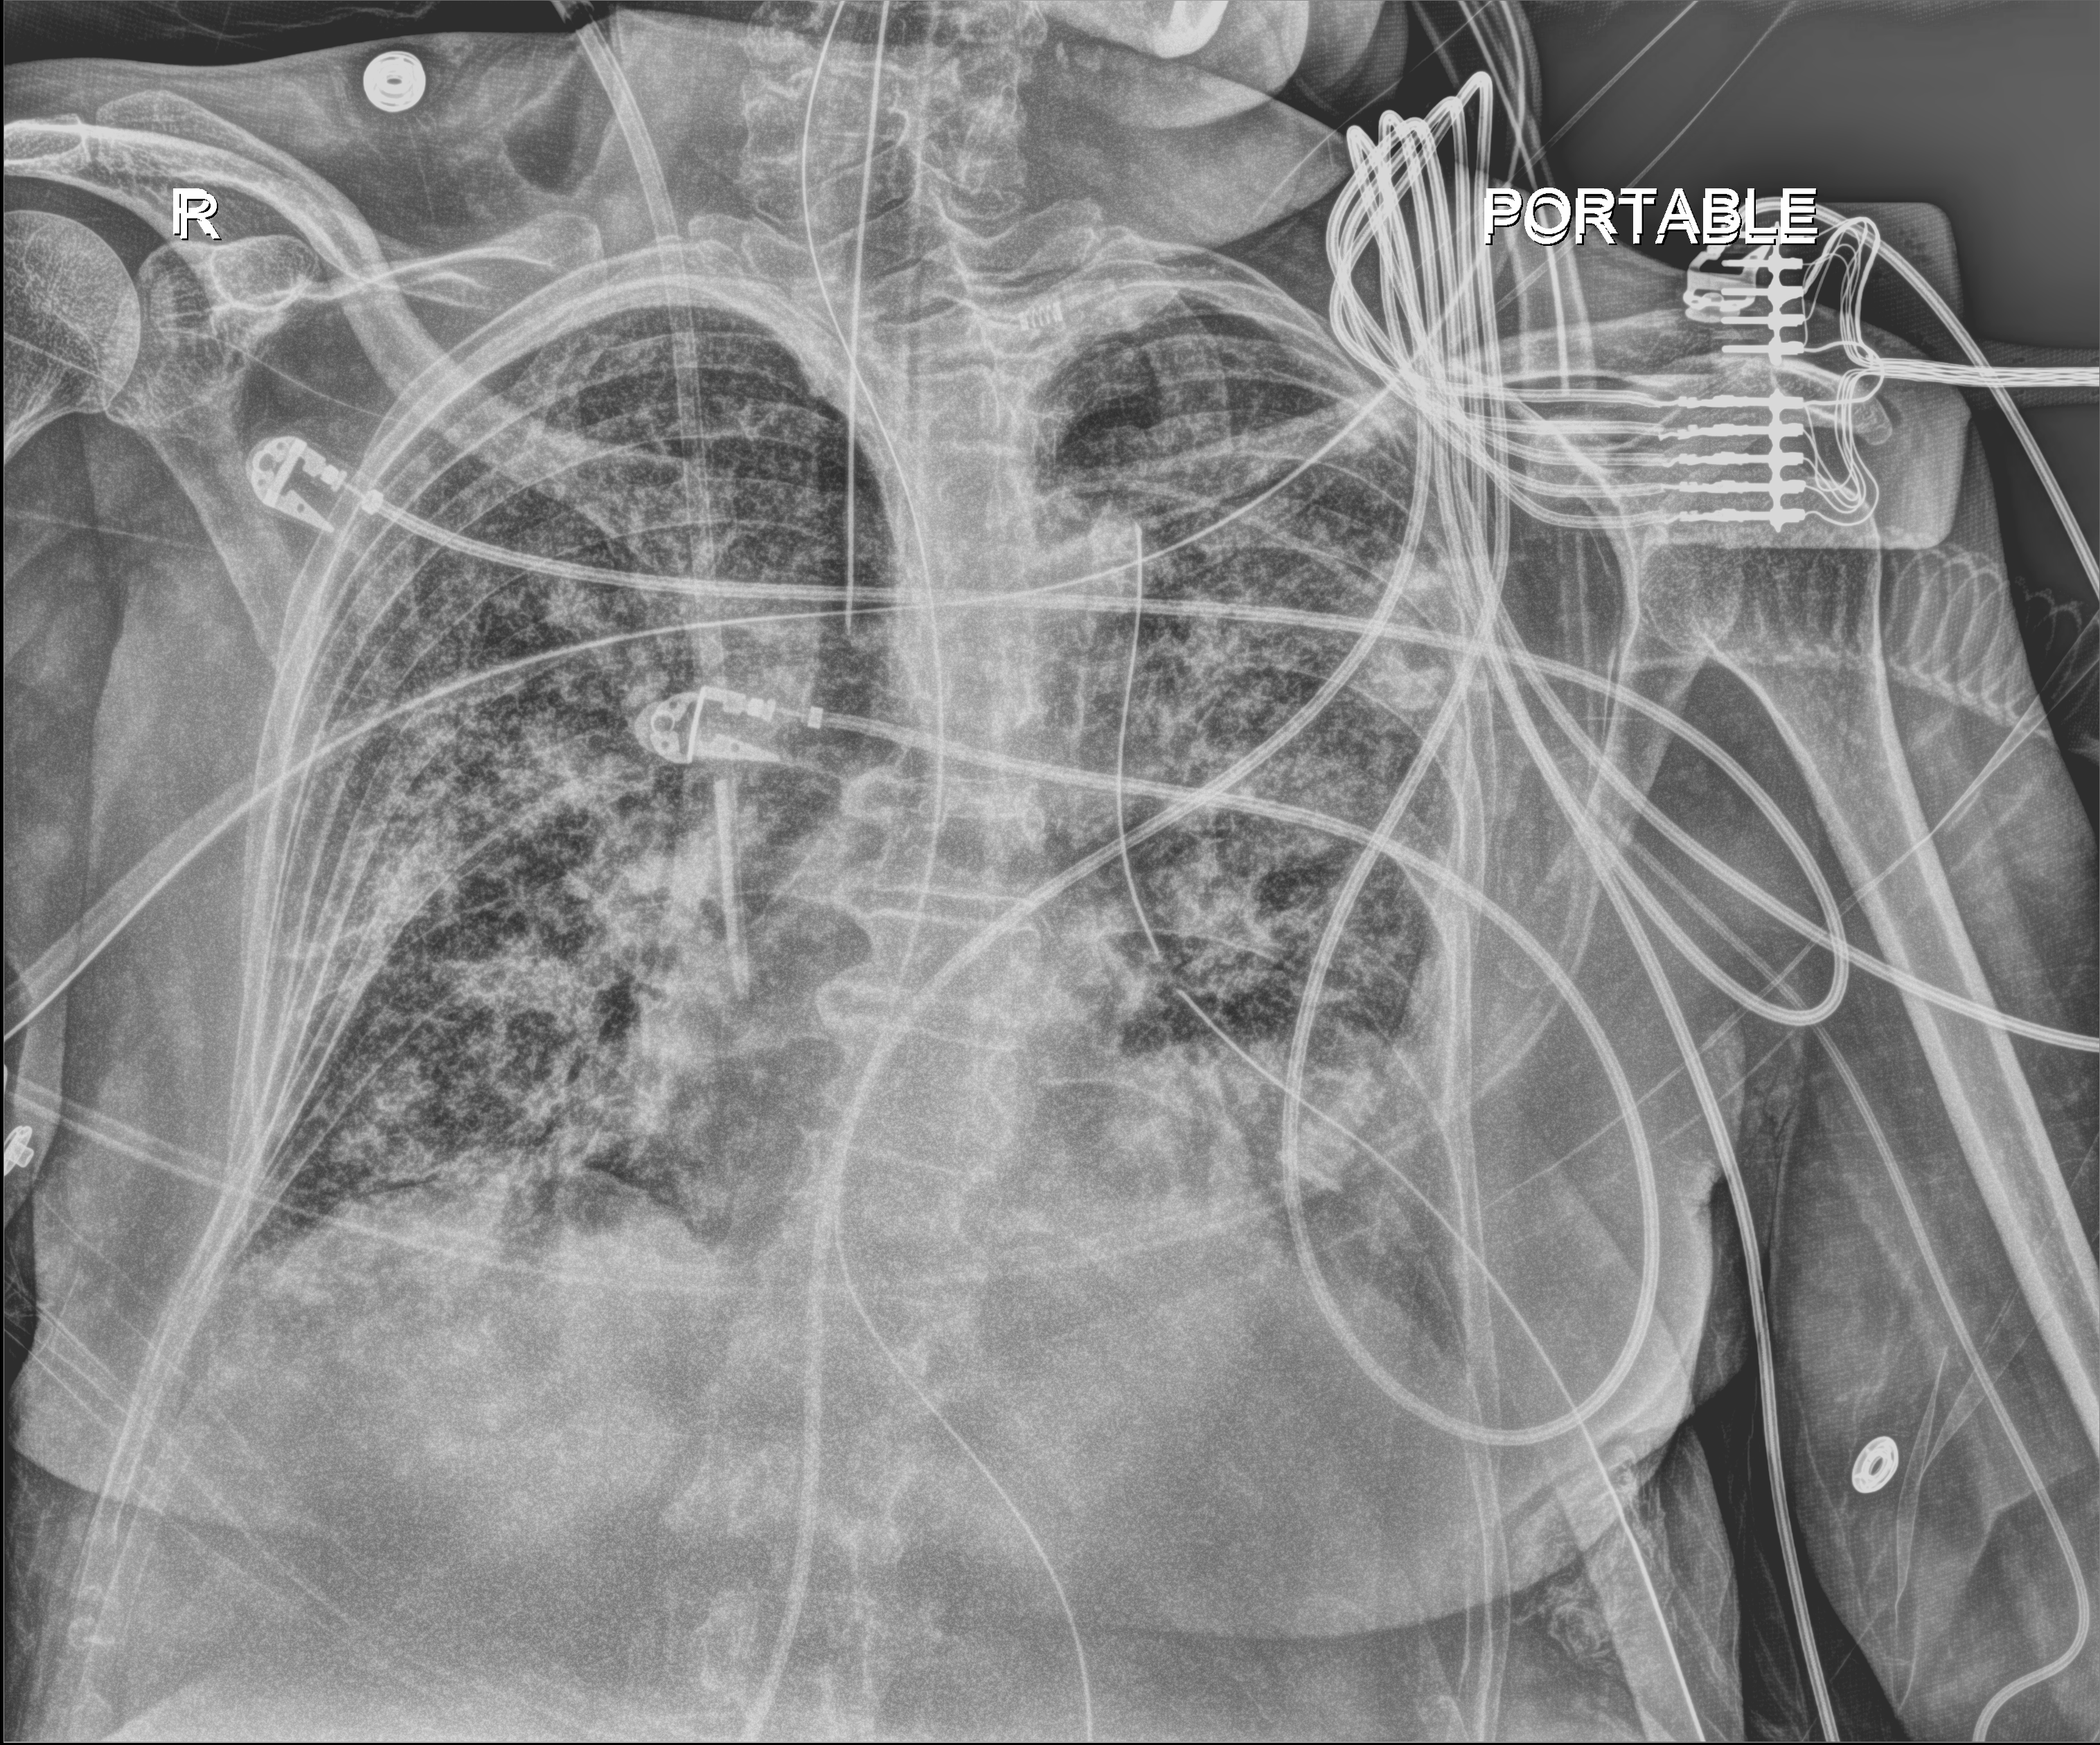
Chest X-ray (portable); anteroposterior (AP) projection. Patient hospitalised with COVID-19; female, aged 75–90 years.
Admission-level facts for this patient (not findings on this image; timing relative to this image not recorded): mechanically ventilated during this hospital stay: yes; admitted to intensive care during this hospital stay: yes.